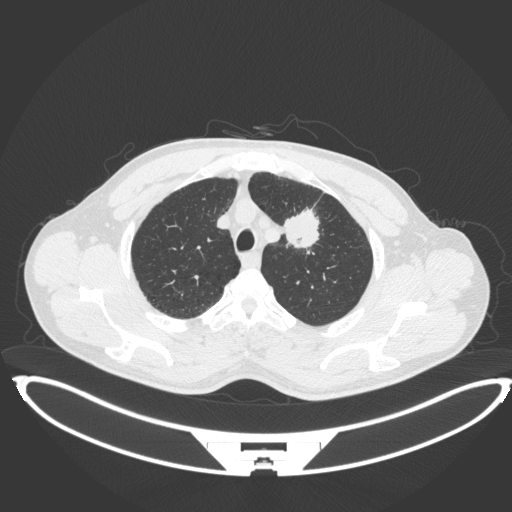
Chest CT, one axial slice; position 358 of 407 along the scan axis; reconstruction kernel B31f; lung window (W 1500 / L -600 HU); 1 mm slice thickness; 512 × 512 image matrix. Patient: male, 60 years. Case-level facts recorded for this patient, not image findings: clinical TNM (as recorded): T2a N0 M0.
Outlined on this slice (rectangle marked by the reading radiologist):
- lung tumour (recorded histology: squamous cell carcinoma): bounding box (x1, y1, x2, y2) in pixels: (283, 205, 322, 254)